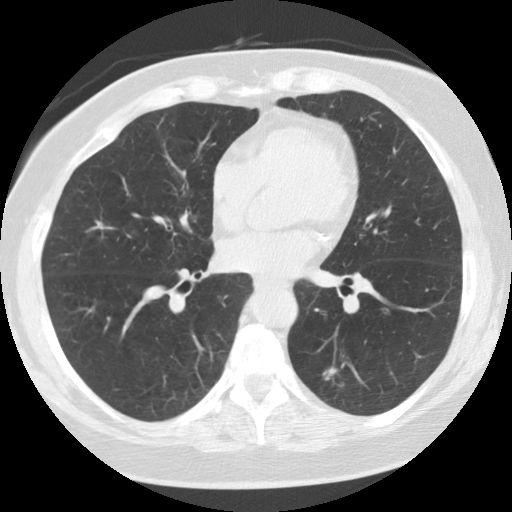
Low-dose screening chest CT, axial slice. Baseline annual screen. Lung window (W 1500 / L -600 HU). 2.5 mm slice thickness. Slice 67 of 115 in the series. 512 × 512 image matrix. Female, age 59 years at enrolment.
Lesion marked by an expert reader, bounding box <290,350,359,415> (left, top, right, bottom; pixels). The screening reader recorded 5 non-calcified nodules or masses ≥4 mm on this exam (right upper lobe, right lower lobe, left lower lobe, right lower lobe, left lower lobe); which of them this box marks is not recorded. Later outcome: lung cancer diagnosed 707 days after this screen — adenocarcinoma, NOS, left lower lobe, poorly differentiated (G3), stage IA (AJCC 6th edition), 15 mm at pathology.